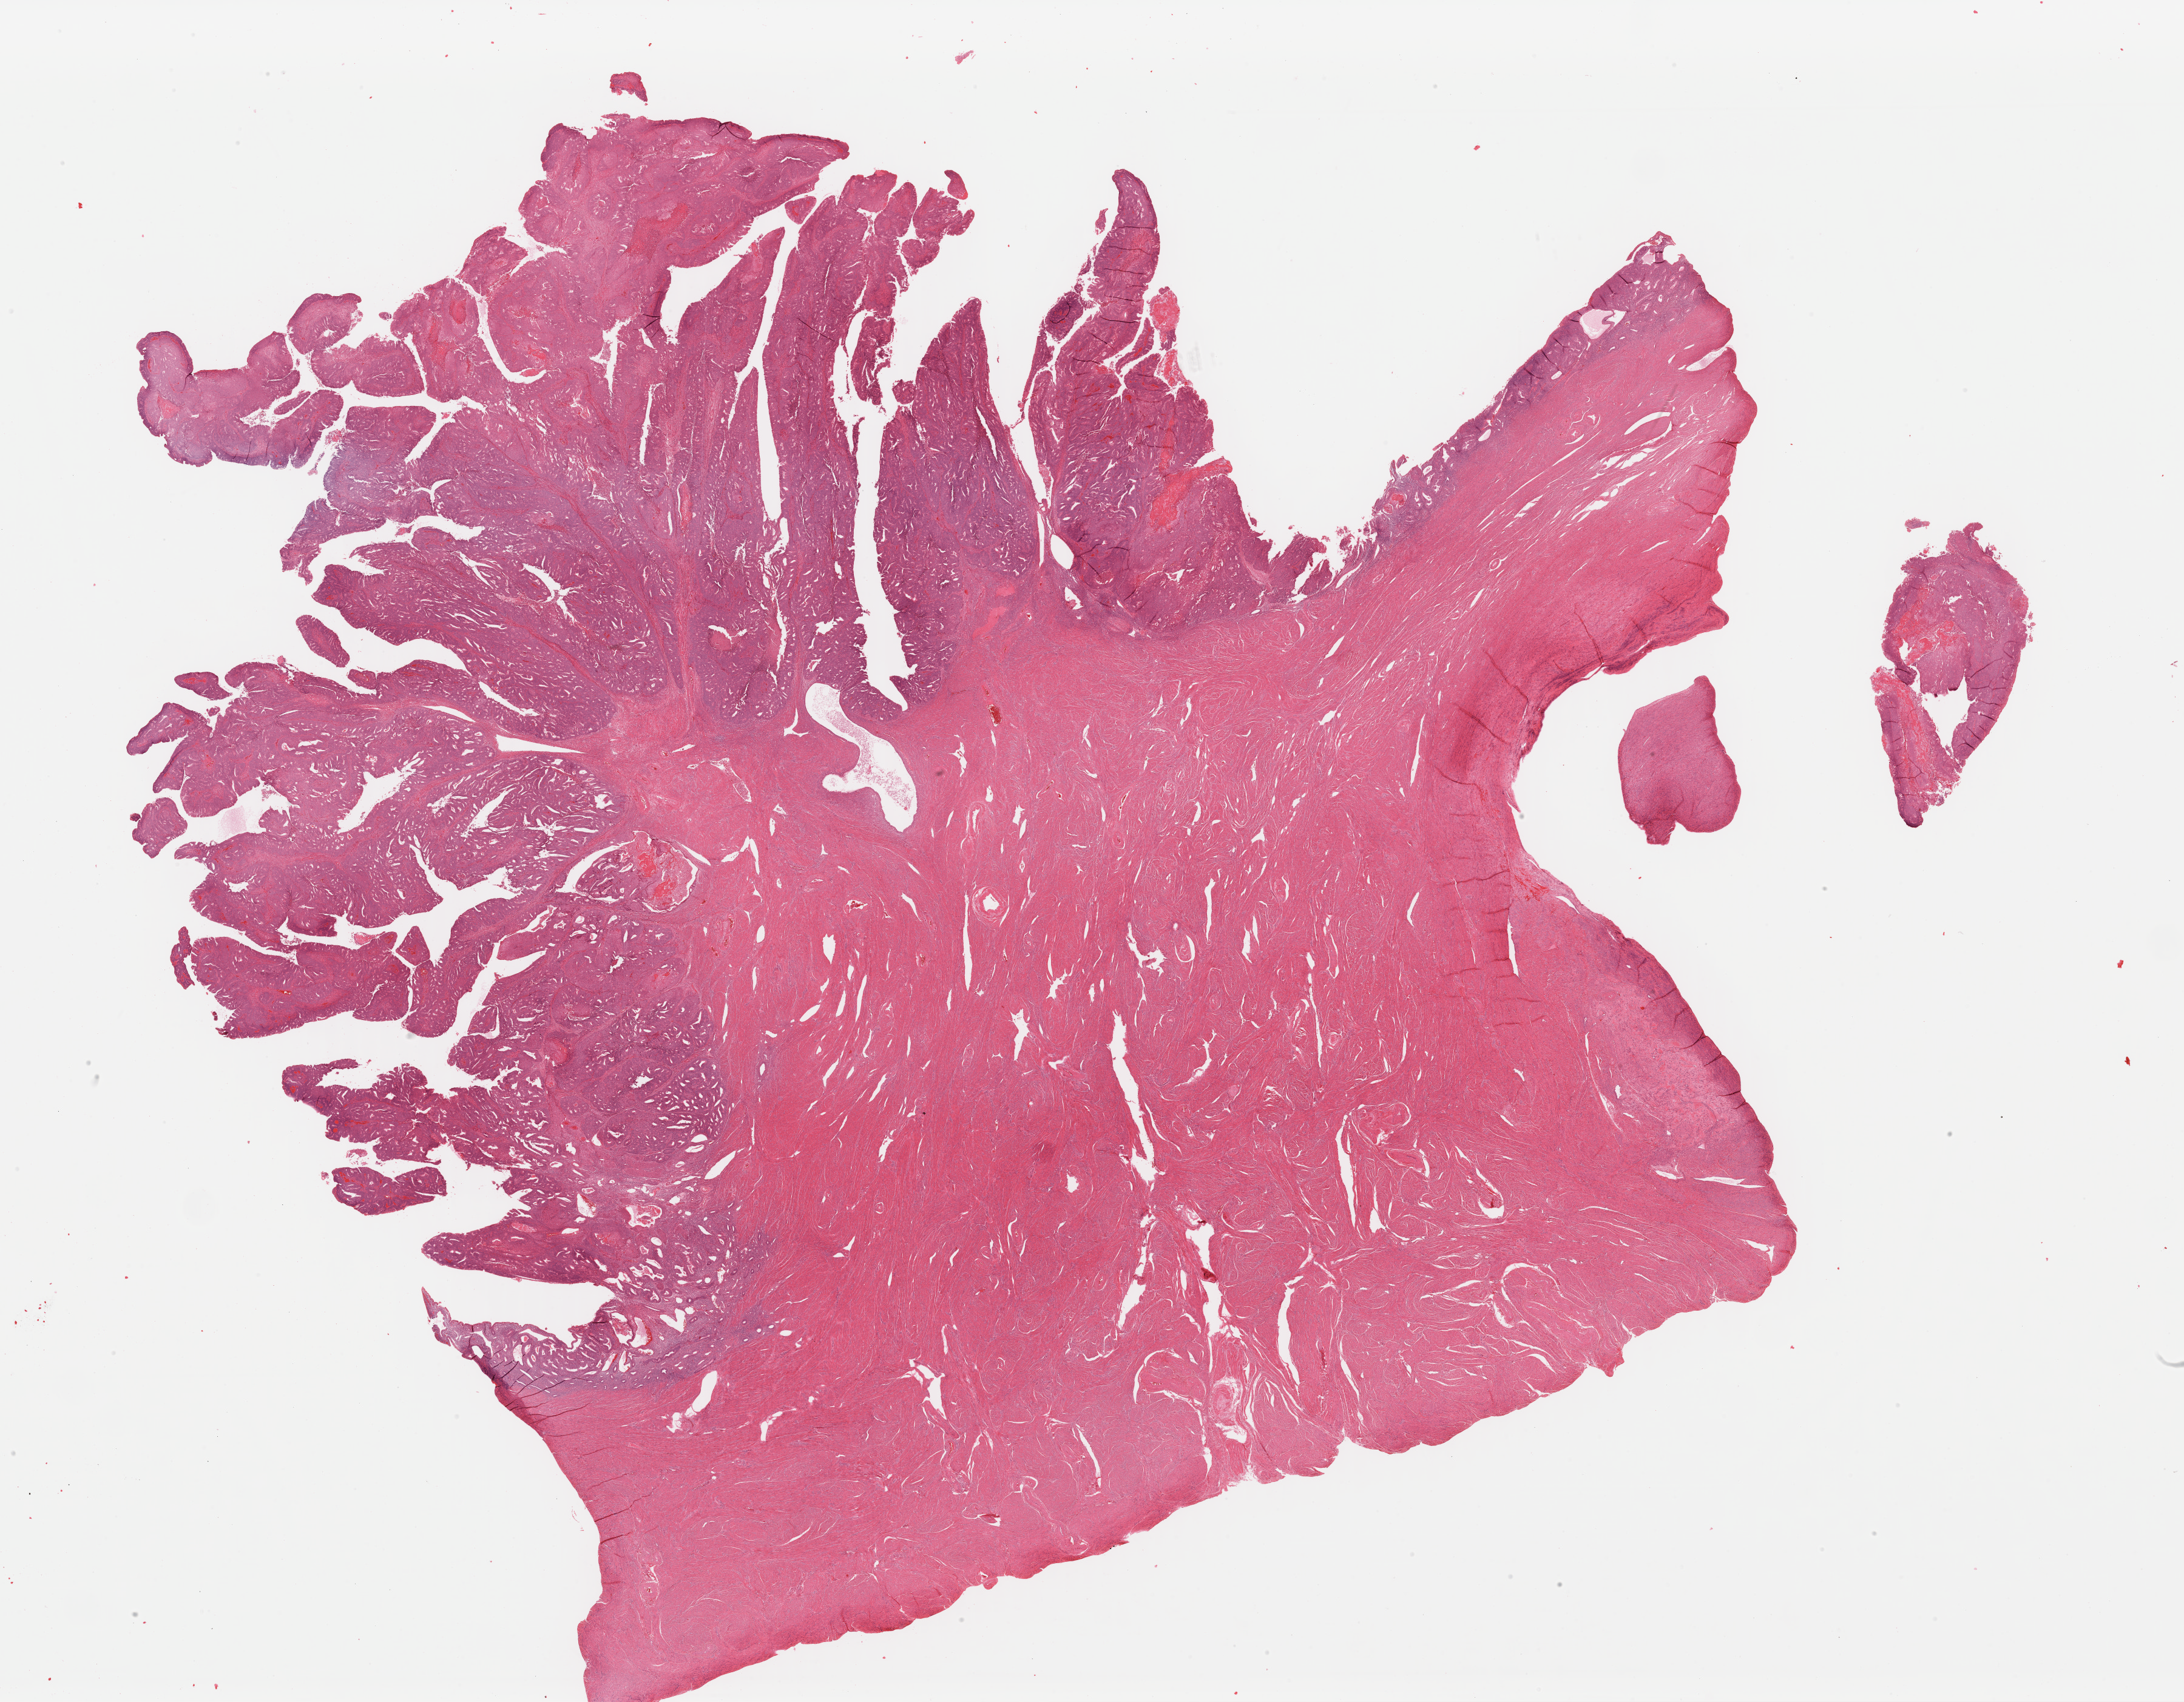
H&E whole-slide image, shown as a low-resolution overview of the whole scanned area (about 28.4 x 22.2 mm, from a 40x scan); formalin-fixed paraffin-embedded (FFPE) diagnostic section; sample: primary tumour, uterus. Patient: female, age at initial diagnosis 53 years. Histologic grade: G1 (well differentiated).
FIGO stage: IB. Histologic diagnosis: Endometrioid adenocarcinoma, NOS.